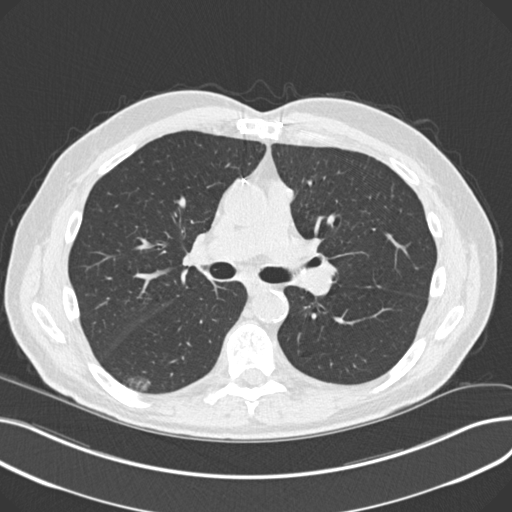
Low-dose screening chest CT, one axial slice; slice 129 of 230 in the series (ordered by position); reconstruction kernel B30f; lung window (W 1500 / L -600 HU); 2 mm slice thickness; 512 × 512 image matrix, field of view 372 × 372 mm.
Outlined on this slice (manually delineated by an expert):
- lesion 1 (nodule, lower lobe of right lung): bounding box (x1, y1, x2, y2) in pixels: (127, 378, 151, 391)